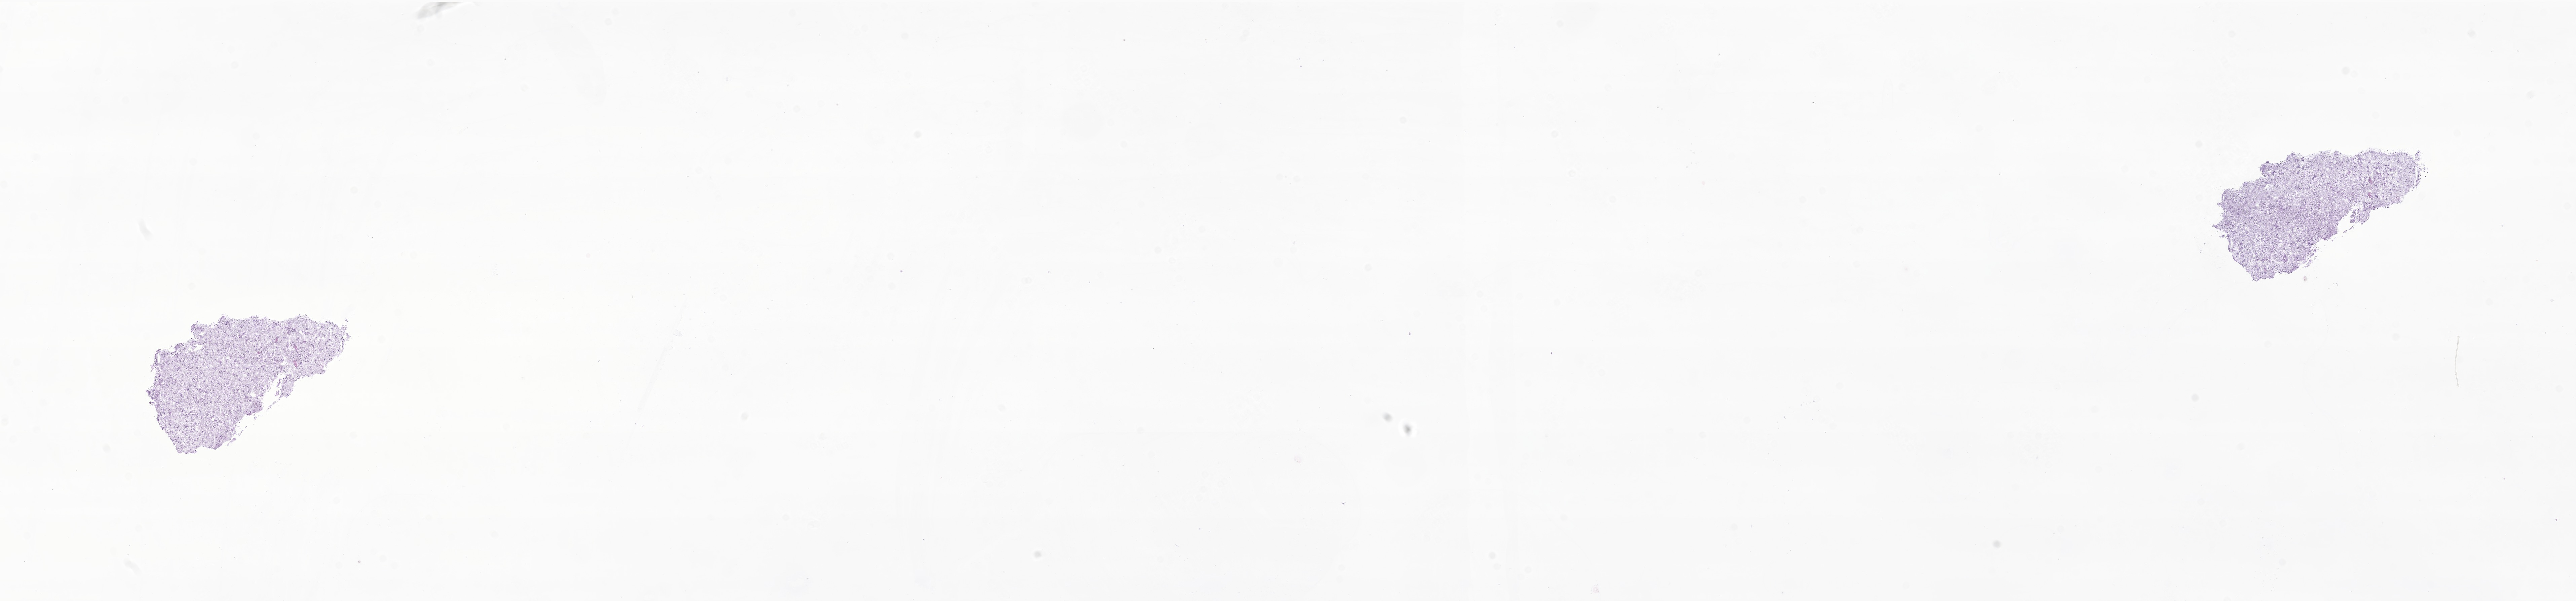
Haematoxylin and eosin whole-slide image of tumor tissue from the parietal lobe, shown as a low-resolution overview of the whole scanned area (about 32.3 x 7.5 mm). Cryosection (OCT / tissue freezing medium). Patient: female, age 86 months (7 years 2 months).
* diagnosis: Glioma, malignant